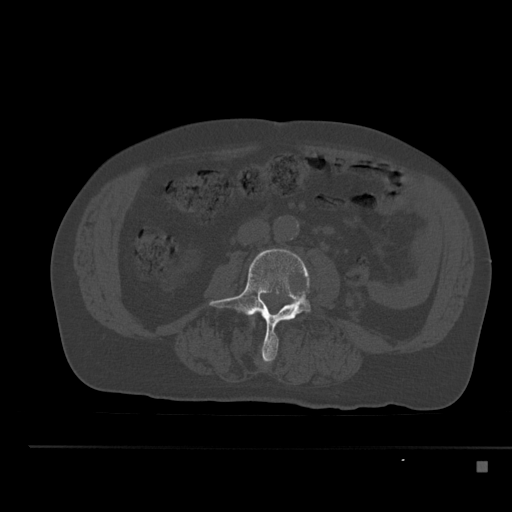
CT including the spine, one axial slice. Position 164 of 517 along the scan axis. Reconstruction kernel Br40s. 120 kVp. Bone window (W 1800 / L 400 HU). 1.5 mm slice thickness. 512 × 512 image matrix, field of view 408 × 408 mm. Male patient, age 70 years. Case-level facts recorded for this patient, not image findings: primary cancer: renal; vertebrae with lytic lesions (as recorded): T4, T6, T10, T12, L3, L4, L5.
Structures marked on this image (semi-automatic segmentation, software-assisted and operator-edited):
- L2 vertebra: bounding box (x1, y1, x2, y2) in pixels: (251, 315, 255, 326)
- L3 vertebra: (209, 249, 311, 362)